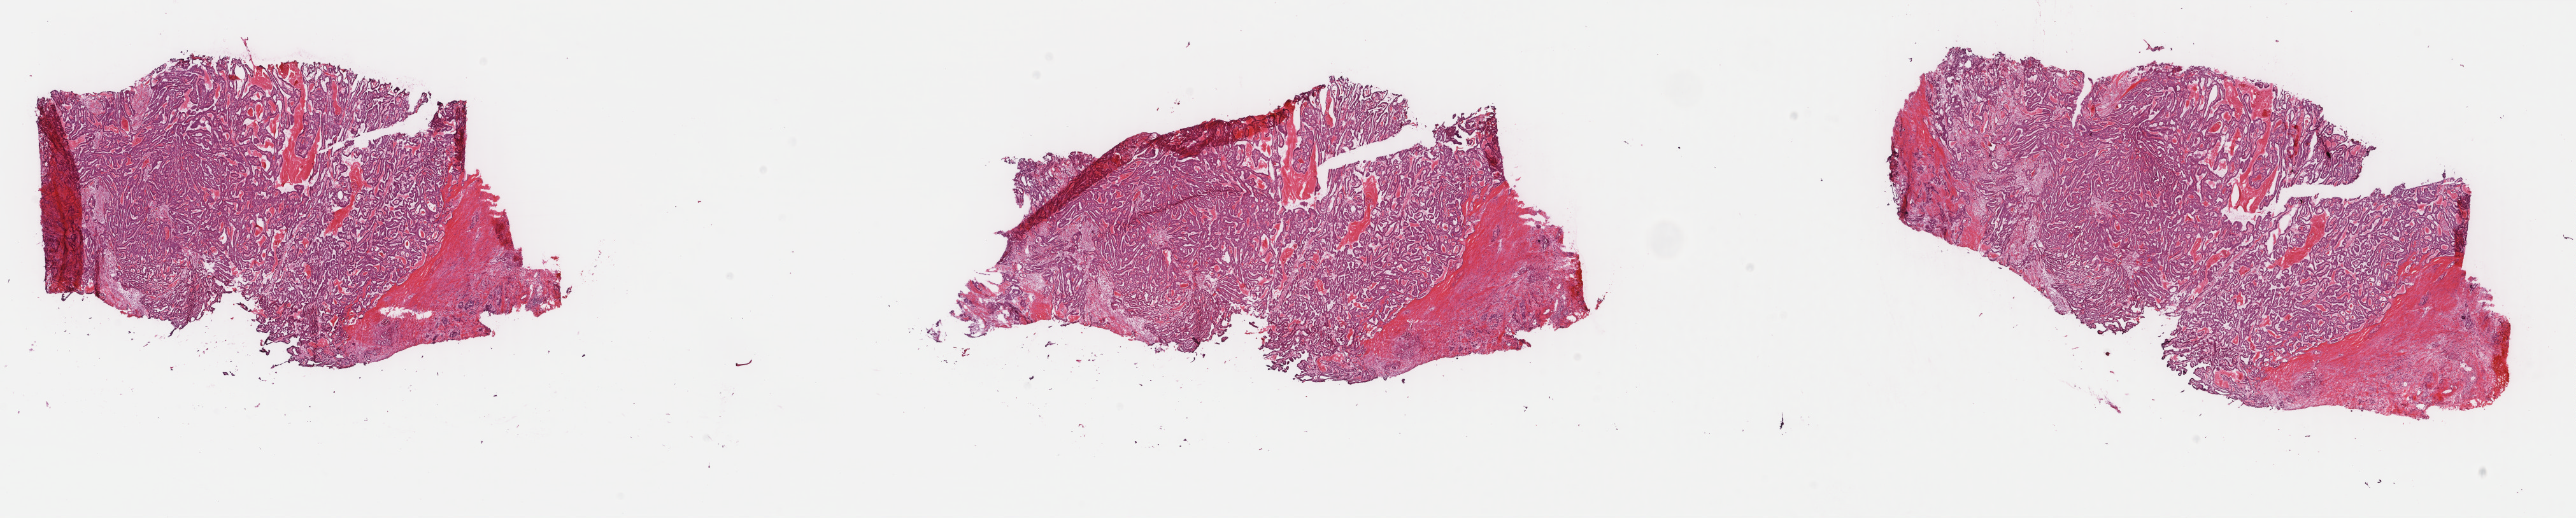
H&E-stained whole-slide image — low-resolution overview of the scanned area, about 32.1 x 6.5 mm (acquisition: 40x scan); frozen section; primary tumour sample from the thyroid. Female patient; age at initial diagnosis 47 years. Pathologist review of this section (percent, as recorded): tumour cells 85%, tumour nuclei 85%, normal cells 0%, stromal cells 15%, necrosis 0%. Inflammatory infiltration, as recorded: lymphocyte infiltration 2%, monocyte infiltration 0%, neutrophil infiltration 0%.
AJCC pathologic stage: I (7th edition). Diagnosis: Papillary adenocarcinoma, NOS.